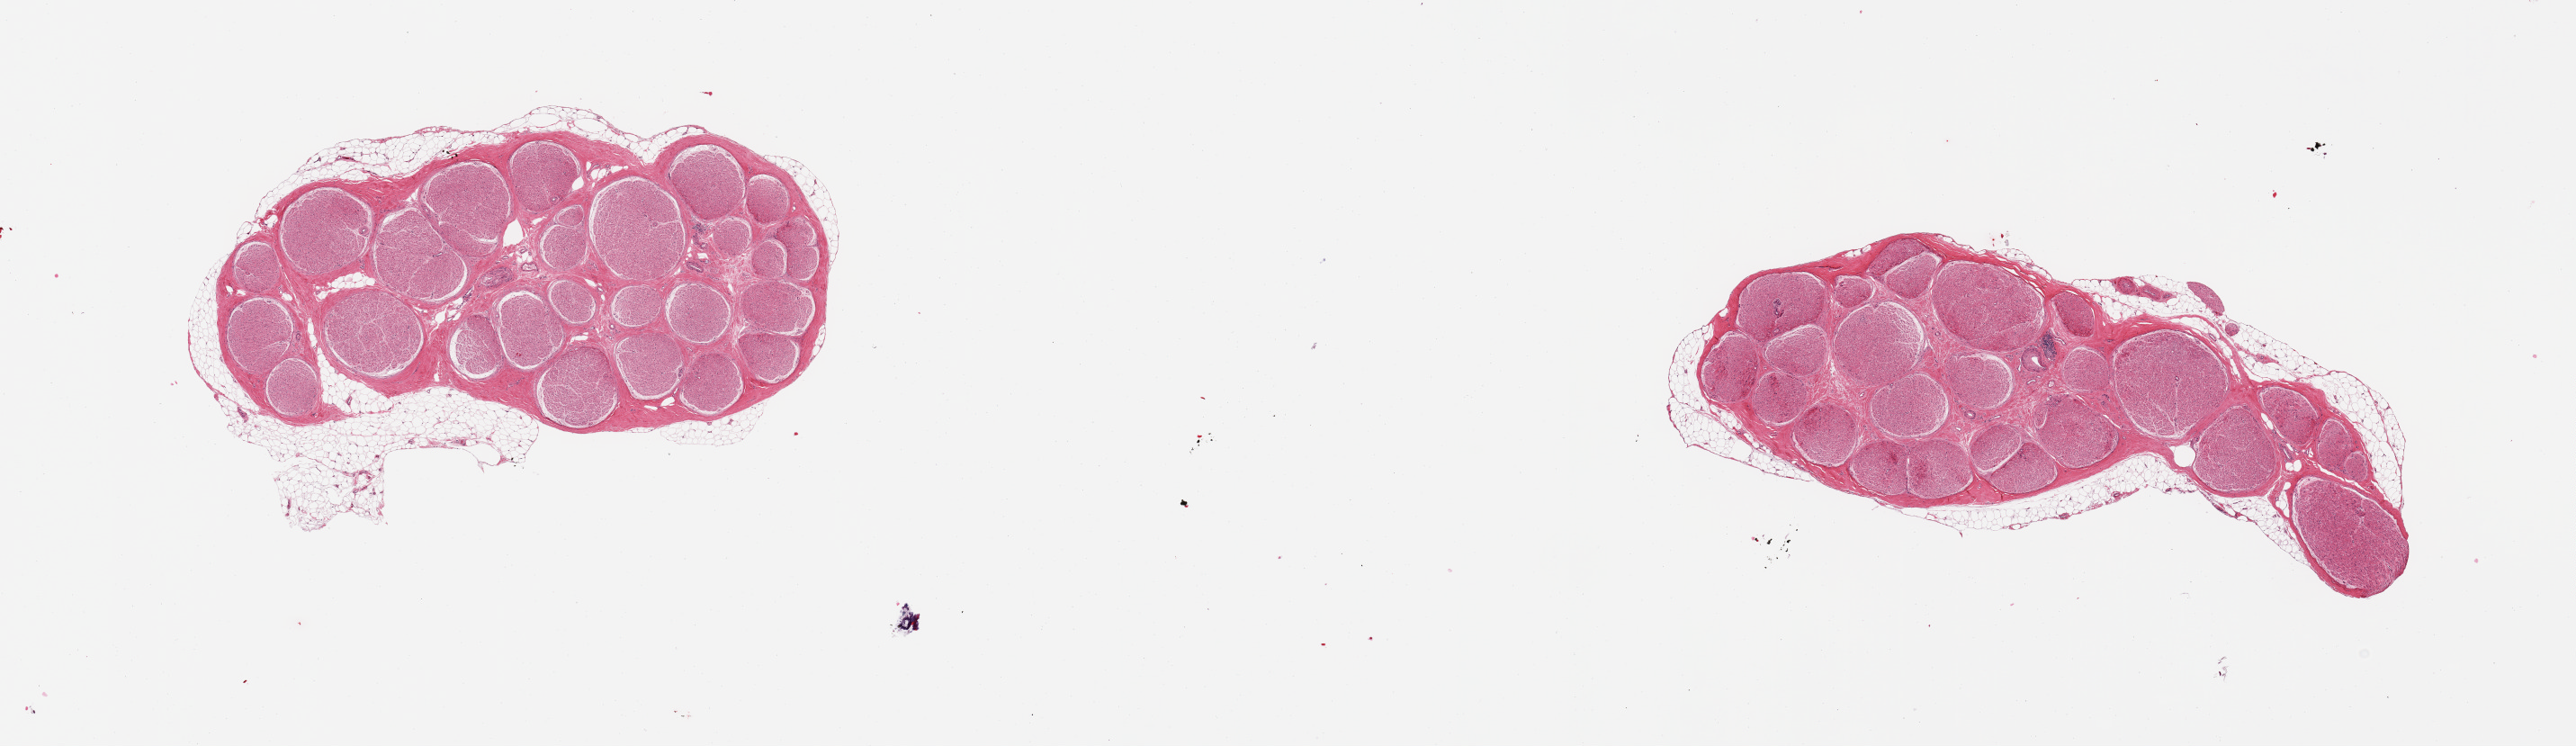
Digitized haematoxylin and eosin-stained section — whole scanned area (about 22.6 x 6.6 mm) shown as a low-resolution overview. PAXgene-fixed paraffin-embedded (PFPE) section. Sampled site (target tissue): tibial nerve. Tissue donor sample. Donor: male.
• review note (as recorded): 2 pieces, trace rim of adherent fat, ~0.2mm